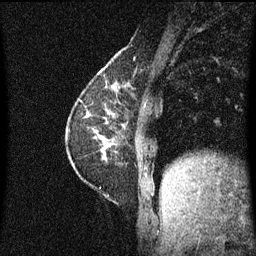
Breast MRI (dynamic contrast-enhanced), one sagittal slice; slice 18 of 60 in the series (ordered by position); dynamic contrast-enhanced series, image 2 of 3 at this slice position (ordered by acquisition); 1.5 T; TE 4.2 ms, TR 8.4 ms; 2 mm slice thickness; 256 × 256 image matrix, field of view 200 × 200 mm. Female patient, age 60 years.
Annotated regions visible in this slice (semi-automatically segmented with operator editing):
- analysis volume of interest (the breast-tissue region the enhancement analysis was run in; not a lesion): bounding box <69,66,132,191> (left, top, right, bottom; pixels)
- tumour enhancement mask (voxels above the 70 % enhancement threshold inside the analysis volume of interest): <86,70,127,161>